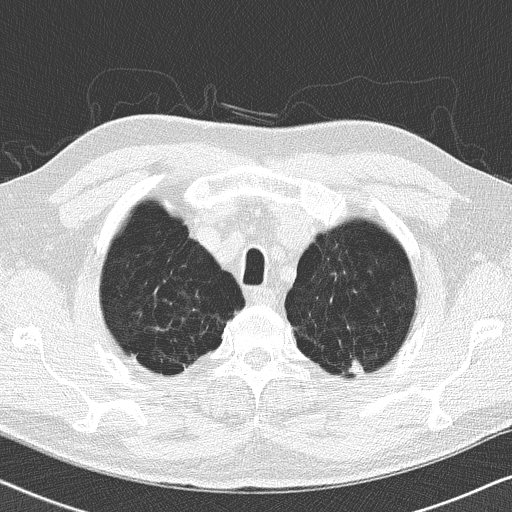
Chest CT (low-dose screening protocol), one axial image; second screening round (one year after baseline); lung window (W 1500 / L -600 HU); 2 mm slice thickness; 120 kVp; slice 21 of 175 in the series; 512 × 512 image matrix, field of view 330 × 330 mm. Male, age 62 years at enrolment.
• Lesion marked by an expert reader, bounding box (x1, y1, x2, y2) in pixels: (335, 351, 376, 387).
• Reader record for this screening exam (exam-level; its link to the box is not recorded): non-calcified nodule or mass ≥4 mm, left upper lobe, 10 × 10 mm, soft tissue attenuation, pre-existing on the prior screen: yes; interval growth: no.
• Official screen result: positive, no significant change: stable abnormalities potentially related to lung cancer, unchanged since the prior screening exam.
• Participant outcome: lung cancer diagnosed 219 days after this screen — adenocarcinoma, NOS, left upper lobe, moderately differentiated (G2), stage IA (AJCC 6th edition), 10 mm at pathology.